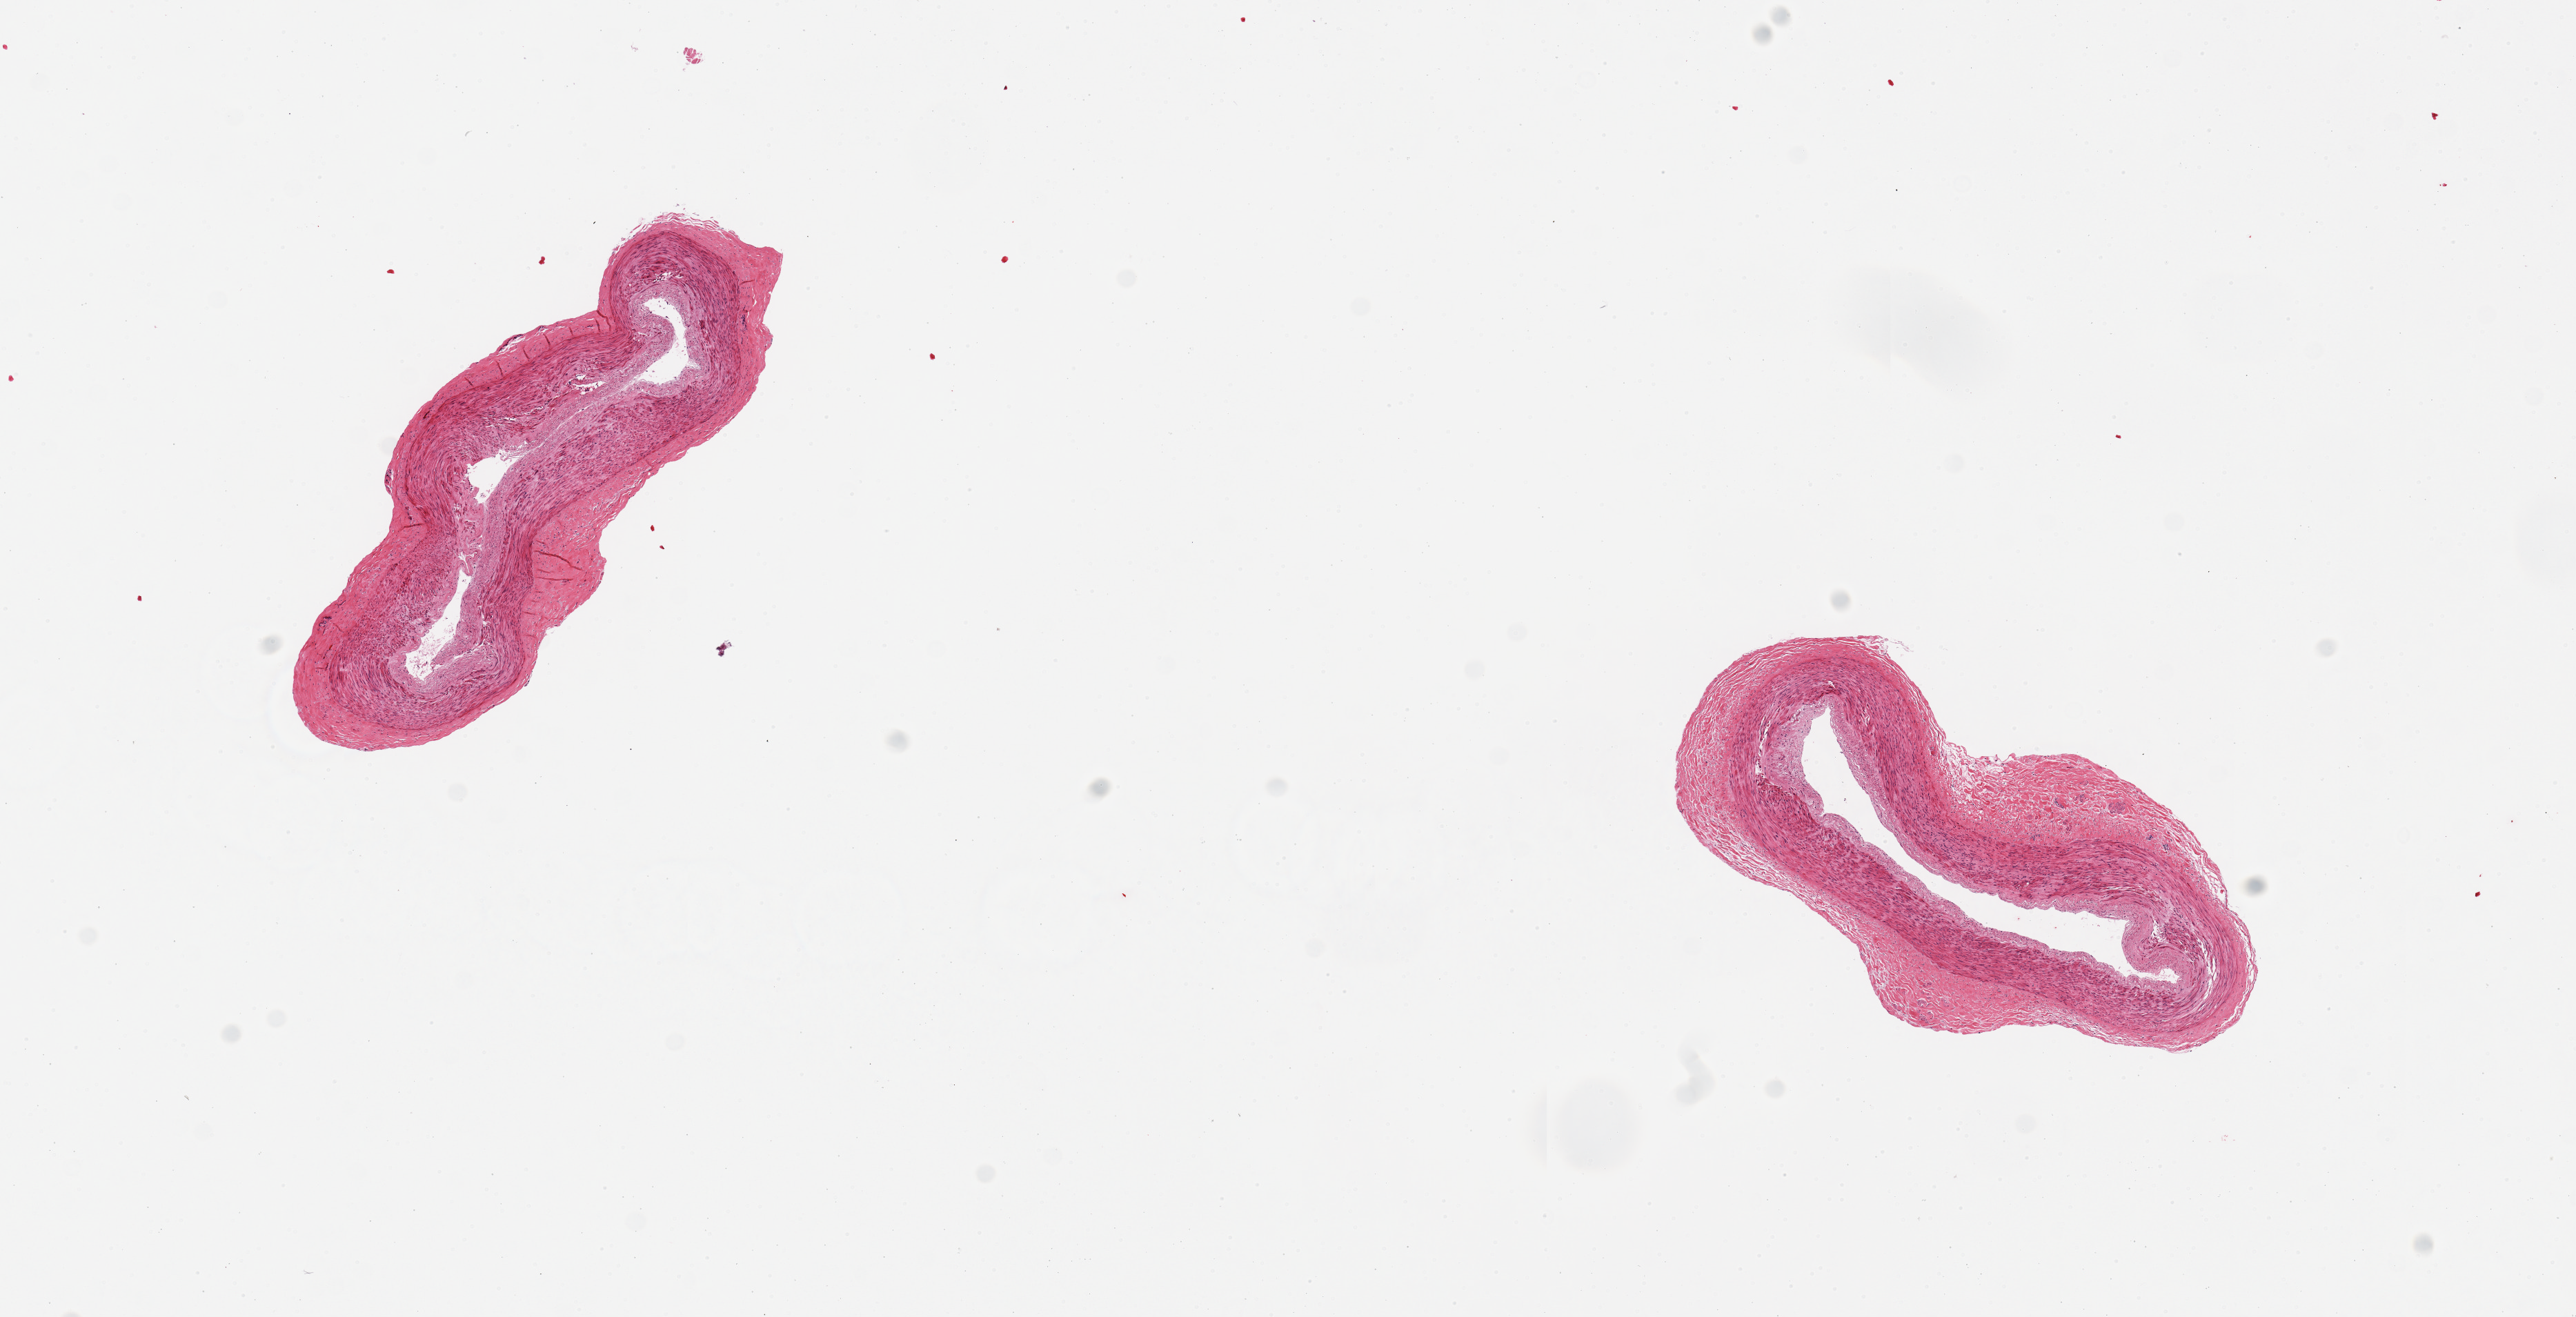
Whole-slide image, hematoxylin and eosin (H&E) stain — low-resolution overview of the scanned area, about 14.8 x 7.5 mm, PAXgene-fixed paraffin-embedded (PFPE) section, section of tibial artery (target tissue), donor tissue sample. Donor sex: male.
- reviewer comment on this tissue sample: 2 pieces, trace fat, good specimens